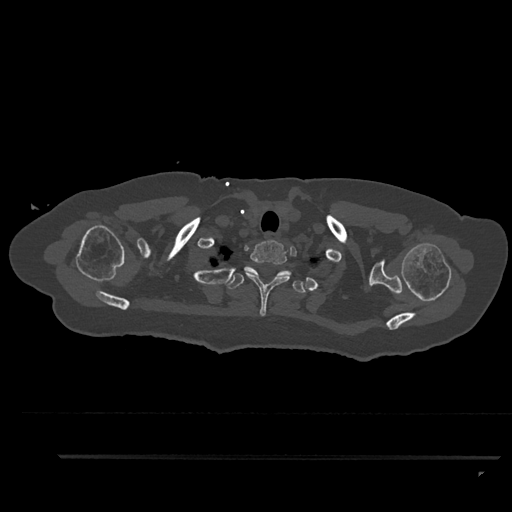
CT including the spine, one axial slice; position 747 of 797 along the scan axis; 120 kVp; bone window (W 1800 / L 400 HU); 0.5 mm slice thickness; 512 × 512 image matrix. Patient: female, 44 years. From the clinical record (not read from this slice): primary cancer: renal; vertebrae with lytic lesions (as recorded): L1.
Annotated regions visible in this slice (semi-automatically segmented with operator editing):
- T1 vertebra: bounding box (x1, y1, x2, y2) in pixels: (242, 240, 291, 316)
- T2 vertebra: (227, 267, 306, 293)